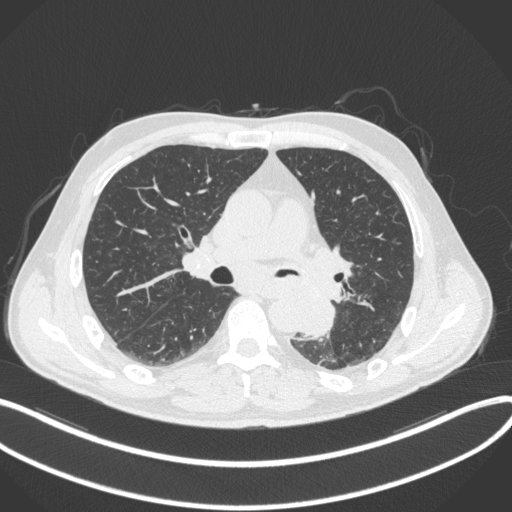
Chest CT, one axial slice; slice 200 of 328 in the series (ordered by position); reconstruction kernel B31f; 120 kVp; lung window (W 1500 / L -600 HU); 512 × 512 image matrix, field of view 400 × 400 mm. Male patient, age 59 years. Case-level facts recorded for this patient, not image findings: clinical TNM (as recorded): T2a N2 M0.
Structures marked on this image (bounding box drawn by a radiologist):
- lung tumour (recorded histology: squamous cell carcinoma): bounding box (x1, y1, x2, y2) in pixels: (296, 291, 342, 341)